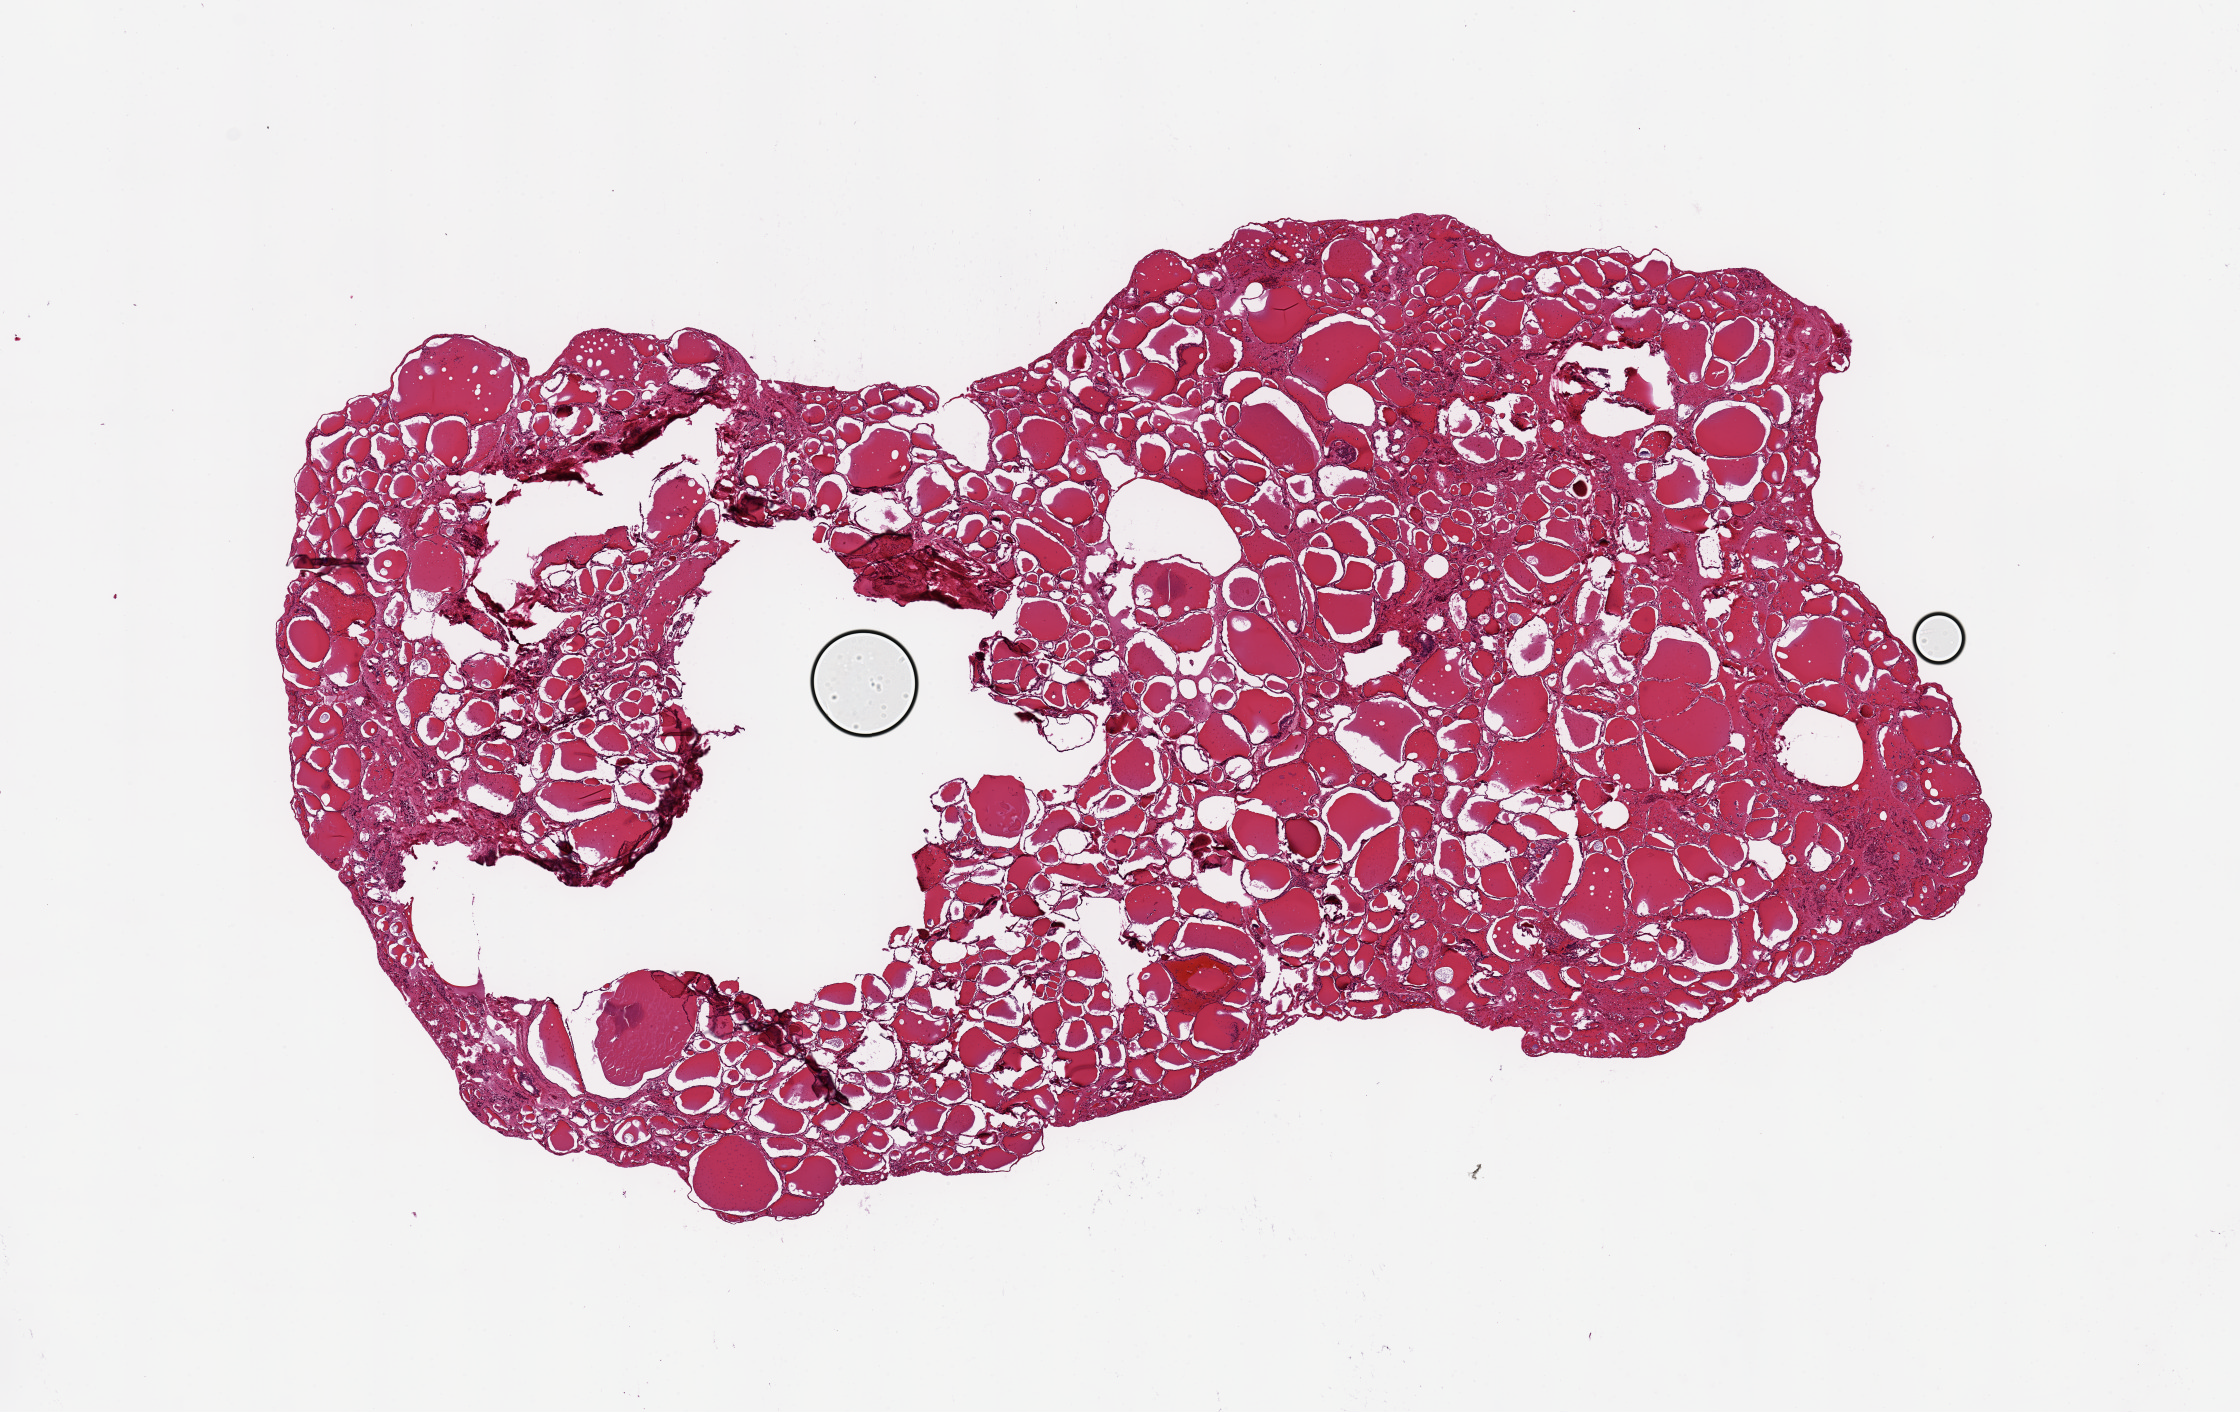
Whole-slide image, hematoxylin and eosin (H&E) stain, shown as a low-resolution overview of the whole scanned area (about 17.7 x 11.2 mm, slide scanned at 20x); PAXgene-fixed paraffin-embedded (PFPE) section; target tissue: thyroid; tissue donor sample. Donor sex: male.
Reviewer comment on this tissue sample: Remarkably well-preserved for endocrine organ.